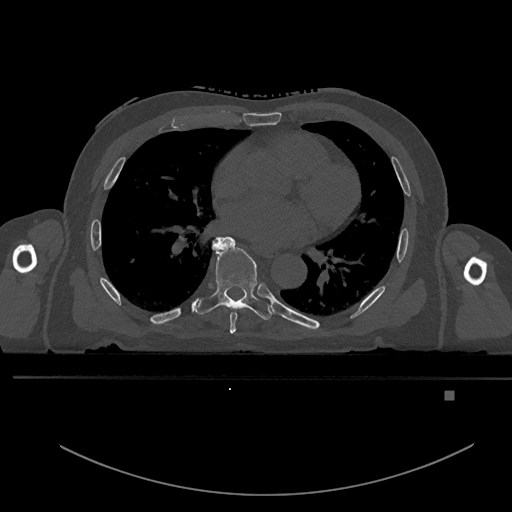
CT including the spine, one axial slice; slice 267 of 969 in the series (ordered by position); bone window (W 1800 / L 400 HU); 0.5 mm slice thickness; 512 × 512 image matrix, field of view 456 × 456 mm. Male patient, age 82 years. From the clinical record (not read from this slice): primary cancer: prostate.
Structures marked on this image (semi-automatically segmented with operator editing):
- T6 vertebra: bounding box (x1, y1, x2, y2) in pixels: (229, 311, 238, 334)
- T7 vertebra: (193, 236, 272, 320)